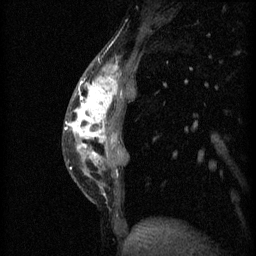
Breast MRI (dynamic contrast-enhanced), one sagittal slice. Slice 15 of 60 in the series (ordered by position). 3 images stored at this slice position (order not interpretable as contrast timing). 1.5 T. TE 4.2 ms, TR 11 ms. 2 mm slice thickness. 256 × 256 image matrix, field of view 180 × 180 mm. Patient: female, 40 years.
Structures marked on this image (semi-automatic segmentation, software-assisted and operator-edited):
- analysis volume of interest (the breast-tissue region the enhancement analysis was run in; not a lesion): bounding box <65,52,136,203> (left, top, right, bottom; pixels)
- tumour enhancement mask (voxels above the 70 % enhancement threshold inside the analysis volume of interest): <66,66,119,171>